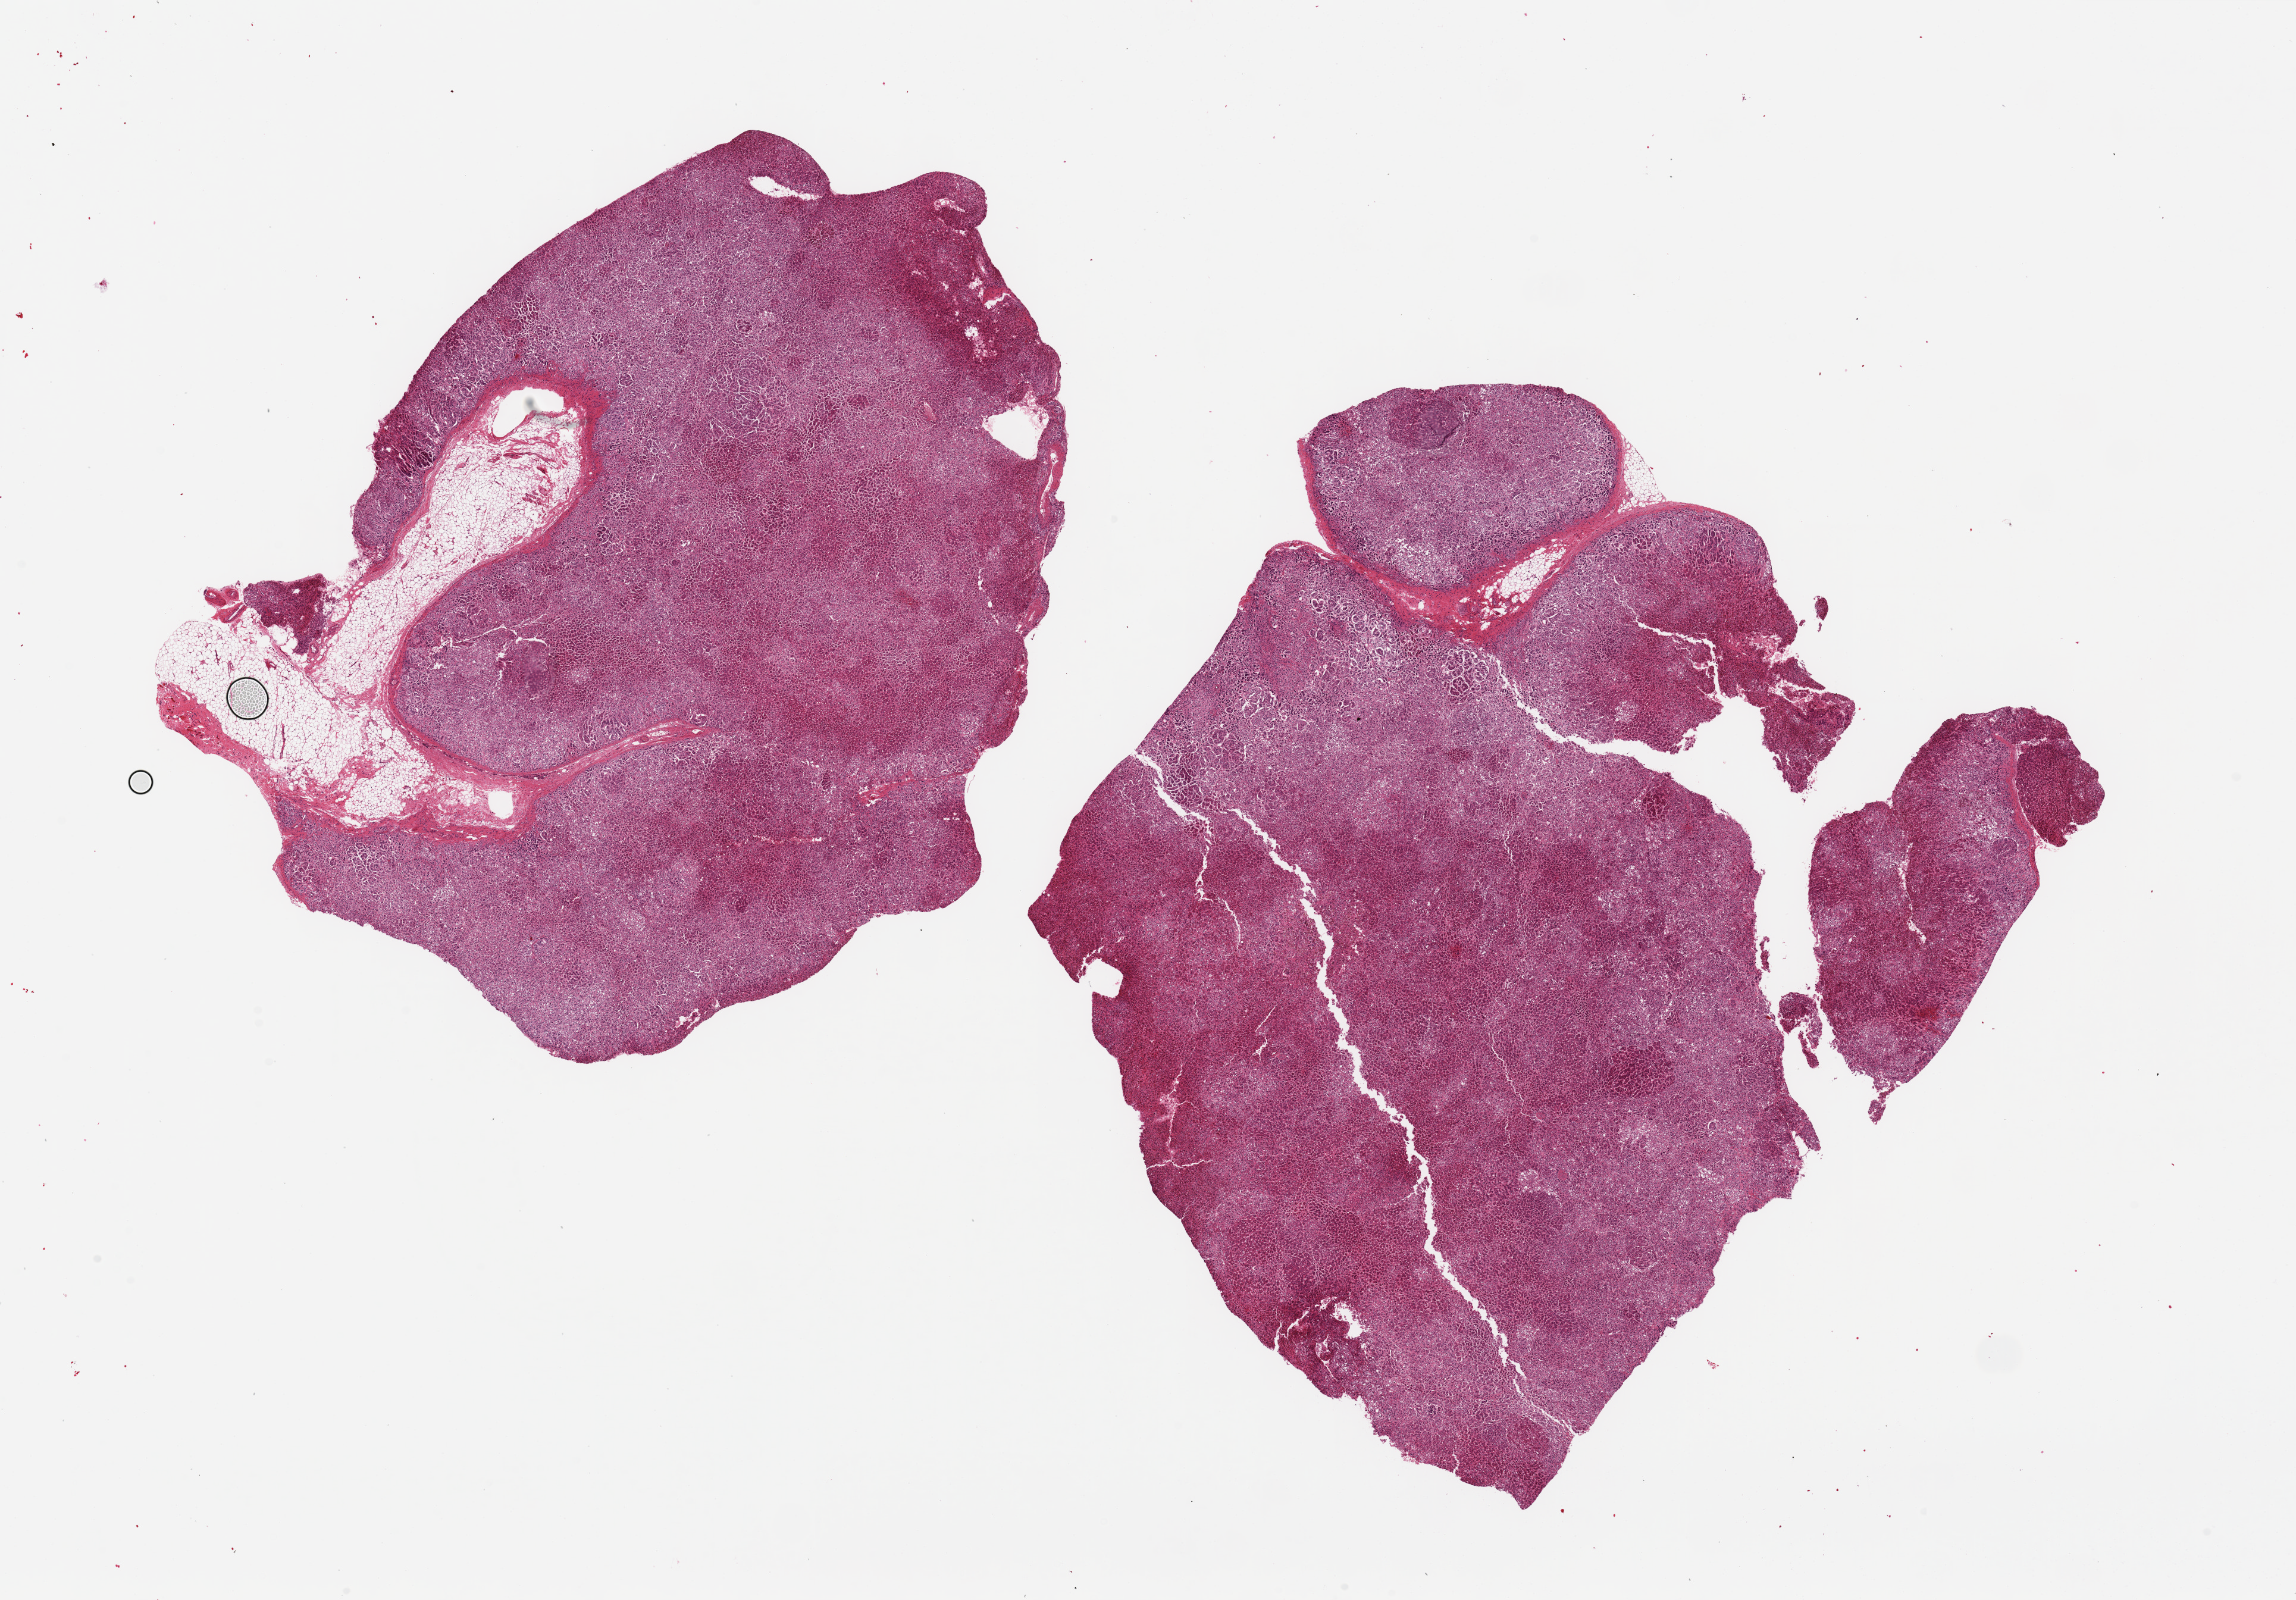
Digitized hematoxylin and eosin (H&E)-stained section, brightfield — shown as a low-resolution overview of the whole scanned area (about 30.5 x 21.3 mm, slide scanned at 20x). PAXgene-fixed, paraffin-embedded tissue. Target tissue: adrenal gland. Donor tissue sample. Donor: male.
- review note (as recorded): 2 pieces ~12x9mm, all cortex, ~5% adherent fat, poorly preserved